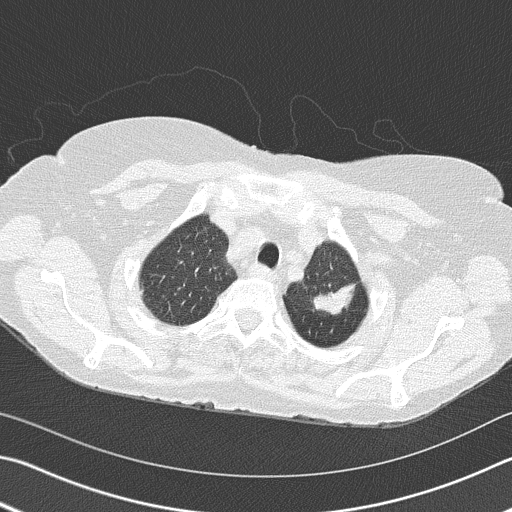
Axial slice from a low-dose chest CT screening exam. Second annual screen. Lung window (W 1500 / L -600 HU). 2 mm slice thickness. Lung (sharp) reconstruction kernel (B50f). Female participant, aged 68 years at enrolment.
Expert-annotated lung lesion, box from (x=289, y=245) to (x=369, y=329) px. The exam's reader record, not a measurement of the box and not confirmed to be the same lesion: non-calcified nodule or mass ≥4 mm, left upper lobe, 4 × 2 mm, spiculated (stellate) margins, soft tissue attenuation, pre-existing on the prior screen: yes; interval growth: yes. Lung cancer was diagnosed 392 days after this screen (after the third annual screen): adenocarcinoma, NOS, left upper lobe, poorly differentiated (G3), stage IB (AJCC 6th edition), 50 mm at pathology.